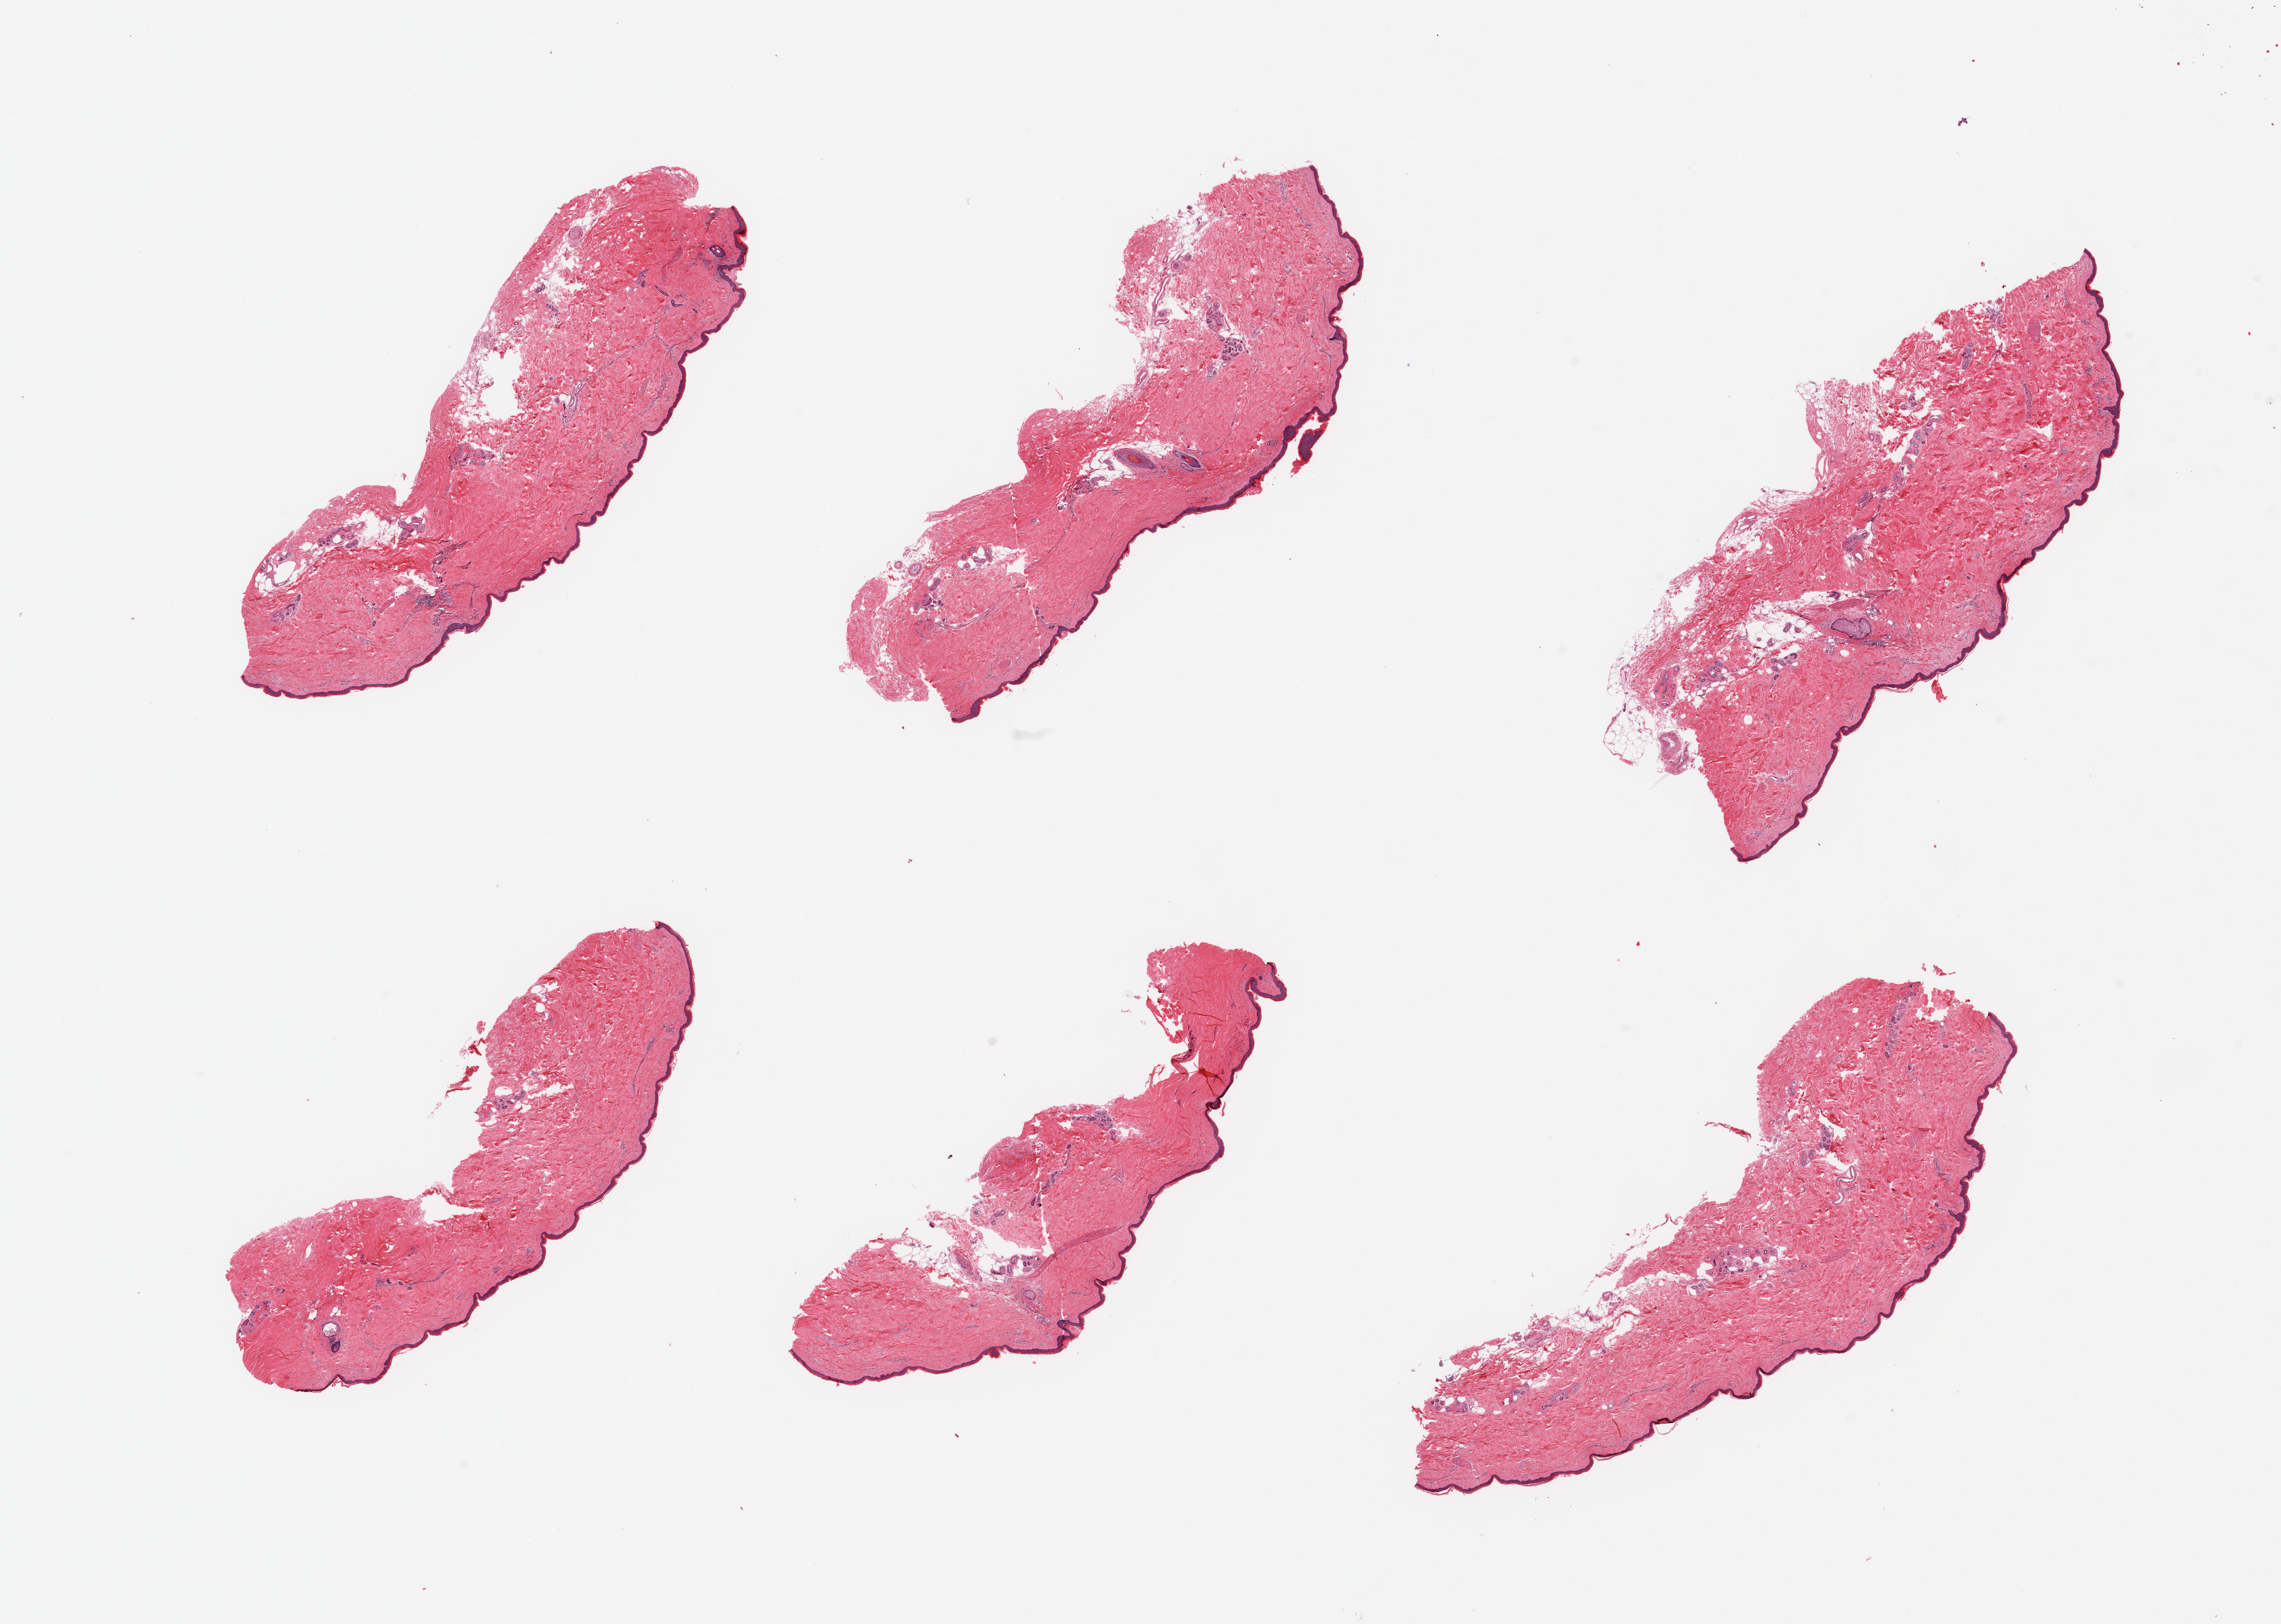
Hematoxylin and eosin (H&E) whole-slide image — low-resolution overview of the scanned area, about 26.6 x 18.9 mm (from a 20x scan), PAXgene-fixed, paraffin-embedded tissue, section of skin of lower leg (target tissue), donor tissue sample. Donor: male.
* reviewer comment on this tissue sample: 6 pieces, trace dermal fat, squamous epithelium is ~35-45 microns